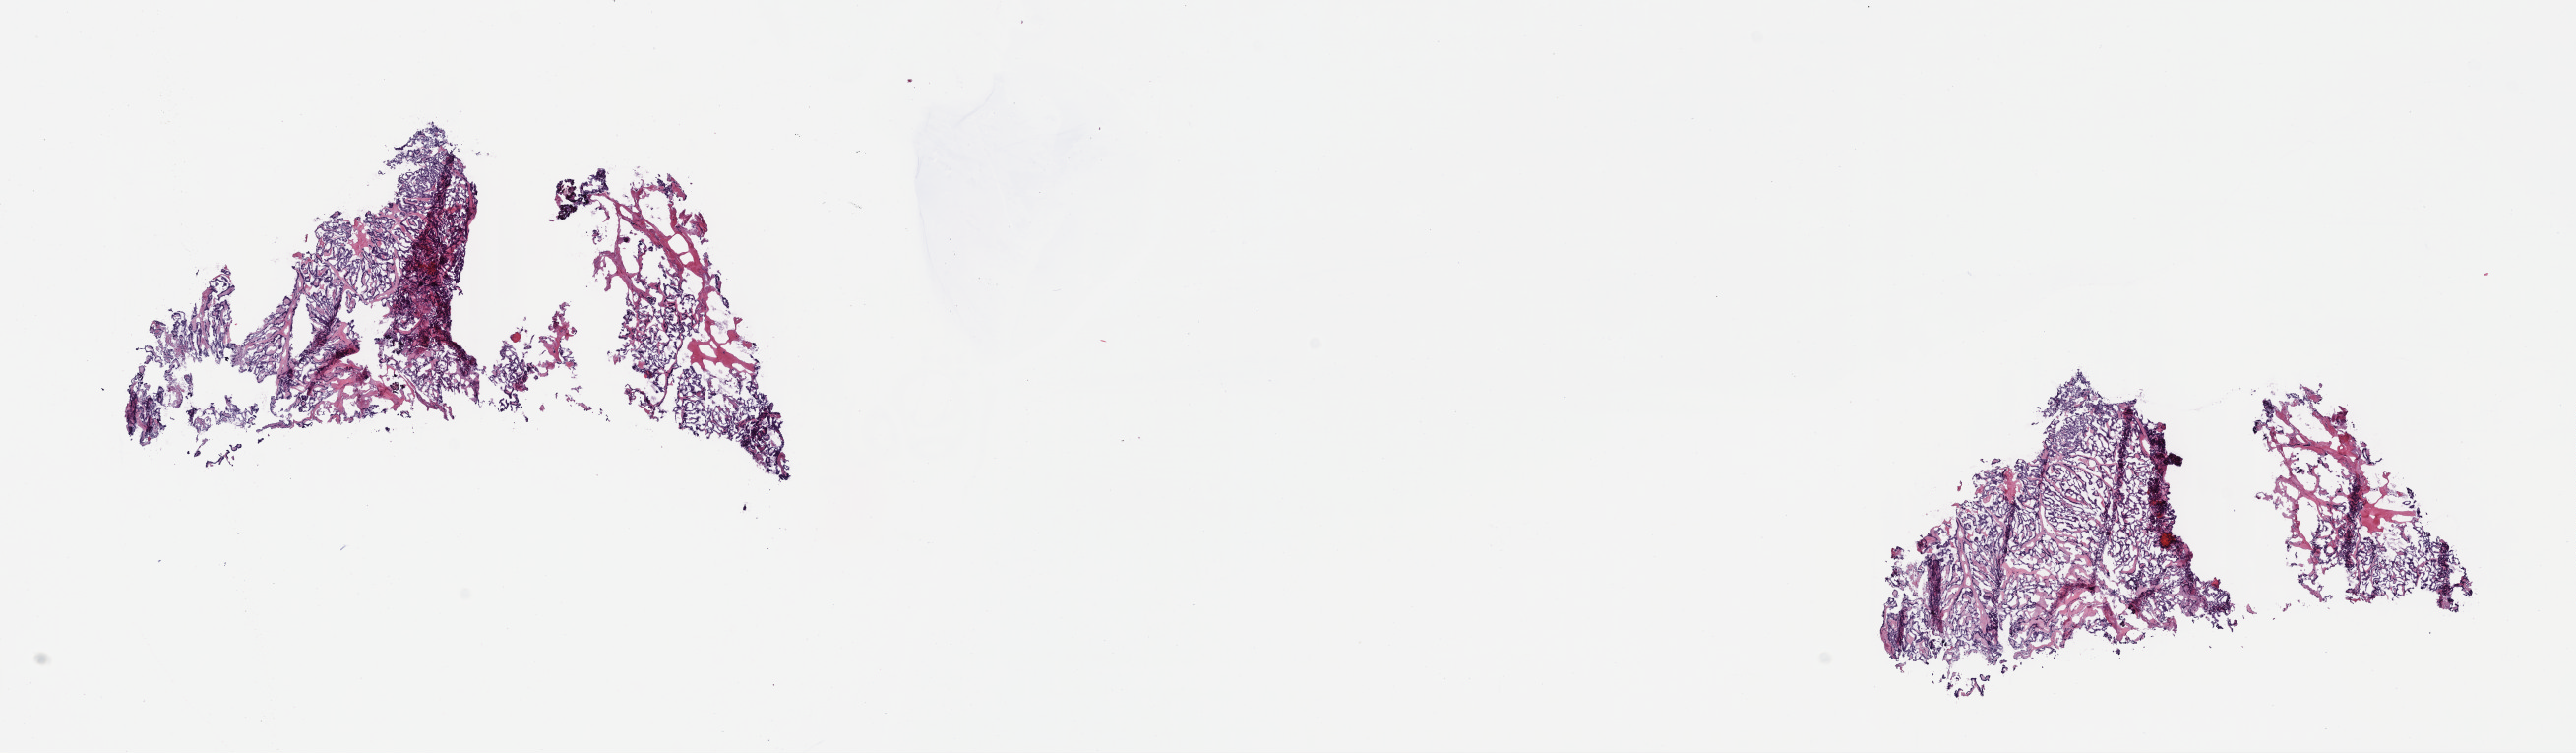
Whole-slide histology image, Hematoxylin and eosin (H&E) stained — a low-resolution overview of the entire scanned area, about 20.6 x 6.0 mm (from a 40x scan). Frozen section from the top of the tissue portion. Sample: primary tumour, thyroid. Patient: male, age at initial diagnosis 74 years. Slide review estimates, as recorded: tumour cells 85%, tumour nuclei 80%, normal cells 0%, stromal cells 15%, necrosis 0%. Infiltration values recorded for this section: lymphocyte infiltration 2%, monocyte infiltration 0%, neutrophil infiltration 0%.
• pathologic diagnosis: Papillary adenocarcinoma, NOS (thyroid gland)
• AJCC pathologic stage: III (6th edition)